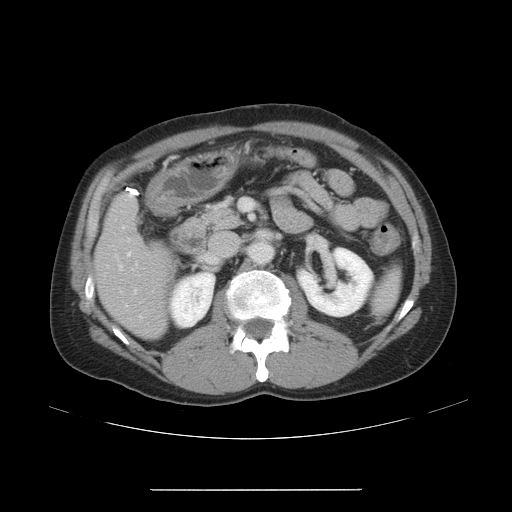
Contrast-enhanced abdominal CT, one axial slice. Slice 22 of 48 in the series (ordered by position). Reconstruction kernel STANDARD. Intravenous contrast given. Soft-tissue window (W 400 / L 40 HU). 5 mm slice thickness. 512 × 512 image matrix, field of view 409 × 409 mm. Male patient, age 56 years. From the clinical record (not read from this slice): diagnosis: colorectal cancer liver metastases, imaged before liver resection; multiple liver metastases: yes; largest metastasis: 1.8 cm.
Structures marked on this image (expert manual segmentation):
- hepatic veins: bounding box [x1, y1, x2, y2] px = [107, 251, 143, 319]
- liver: [96, 198, 170, 337]
- planned liver remnant (the part of the liver to remain after resection): [98, 200, 167, 337]
- portal vein (with intrahepatic branches): [119, 226, 137, 293]